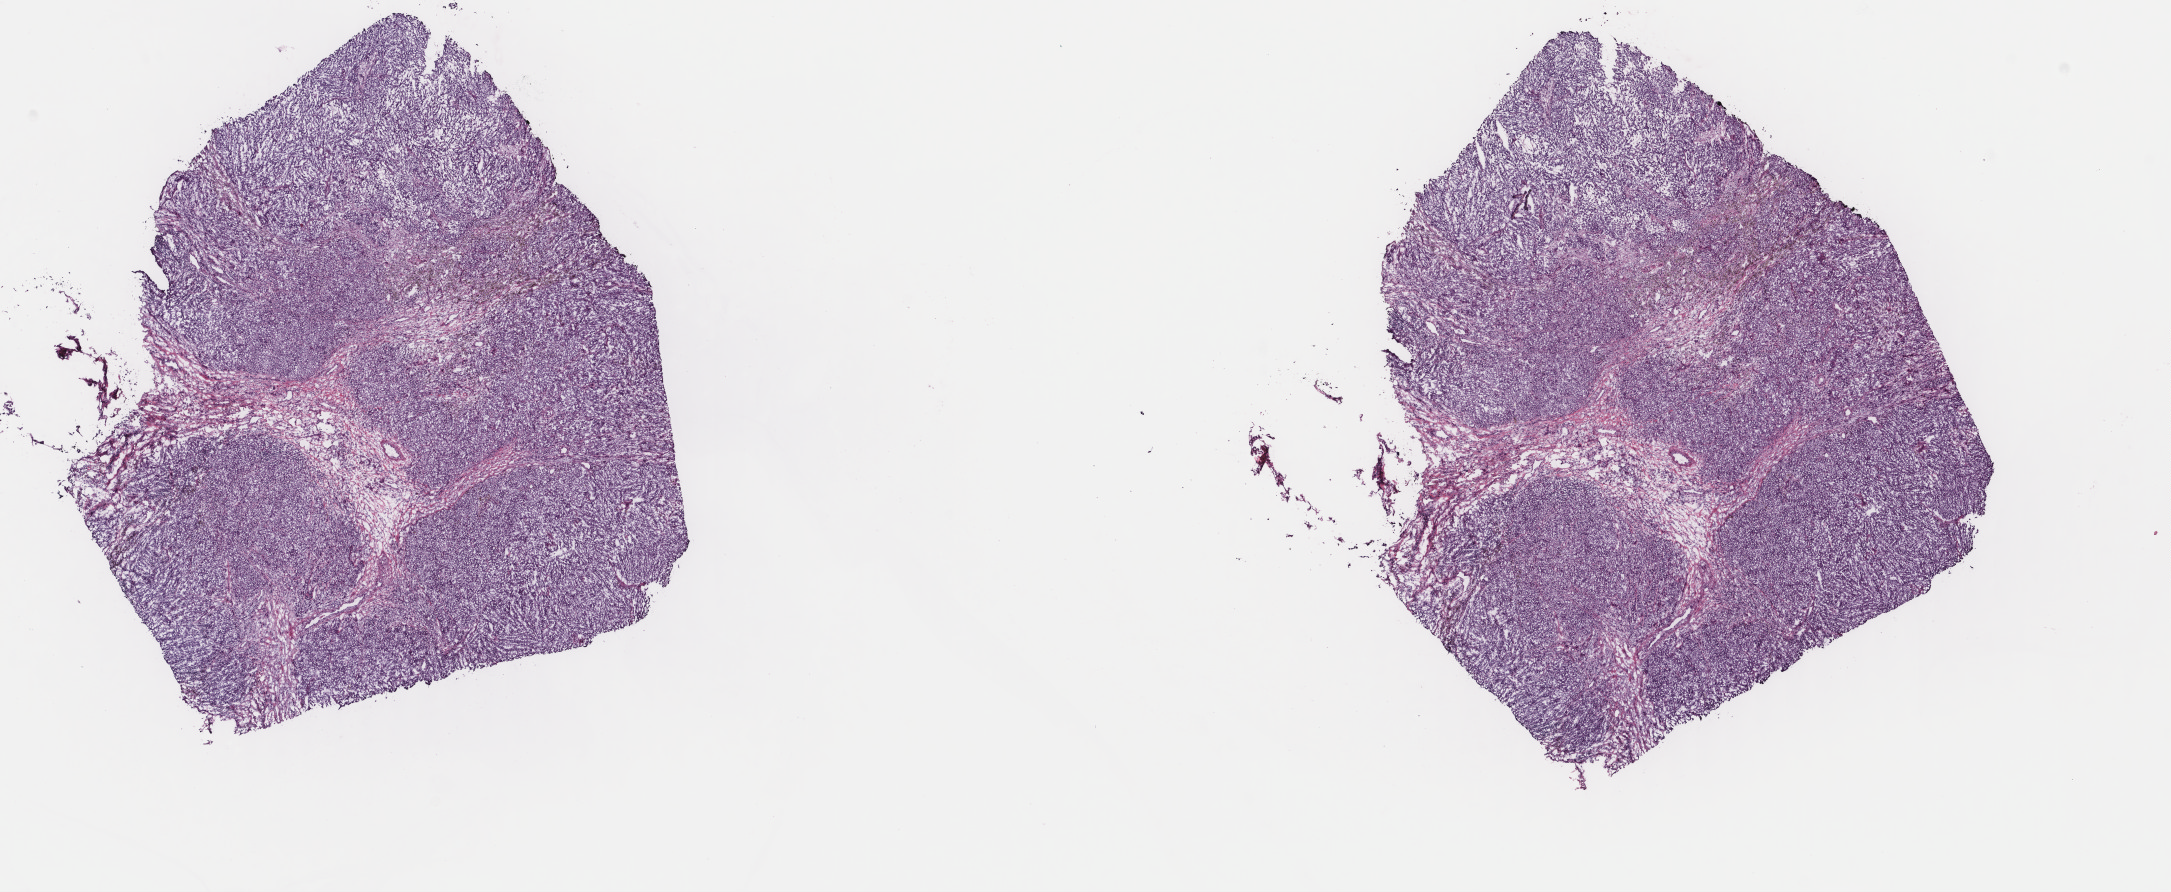
Digitized H&E tissue section (whole slide), low-resolution overview of the scanned area, about 17.2 x 7.1 mm (from a 40x scan), frozen section from the top of the tissue portion, metastatic tumour sample, sampled site not recorded. Male, age 46 years at initial diagnosis. Slide review estimates, as recorded: tumour cells 100%, tumour nuclei 90%.
This section: metastatic tumour tissue. Patient diagnosis: Malignant melanoma, NOS.